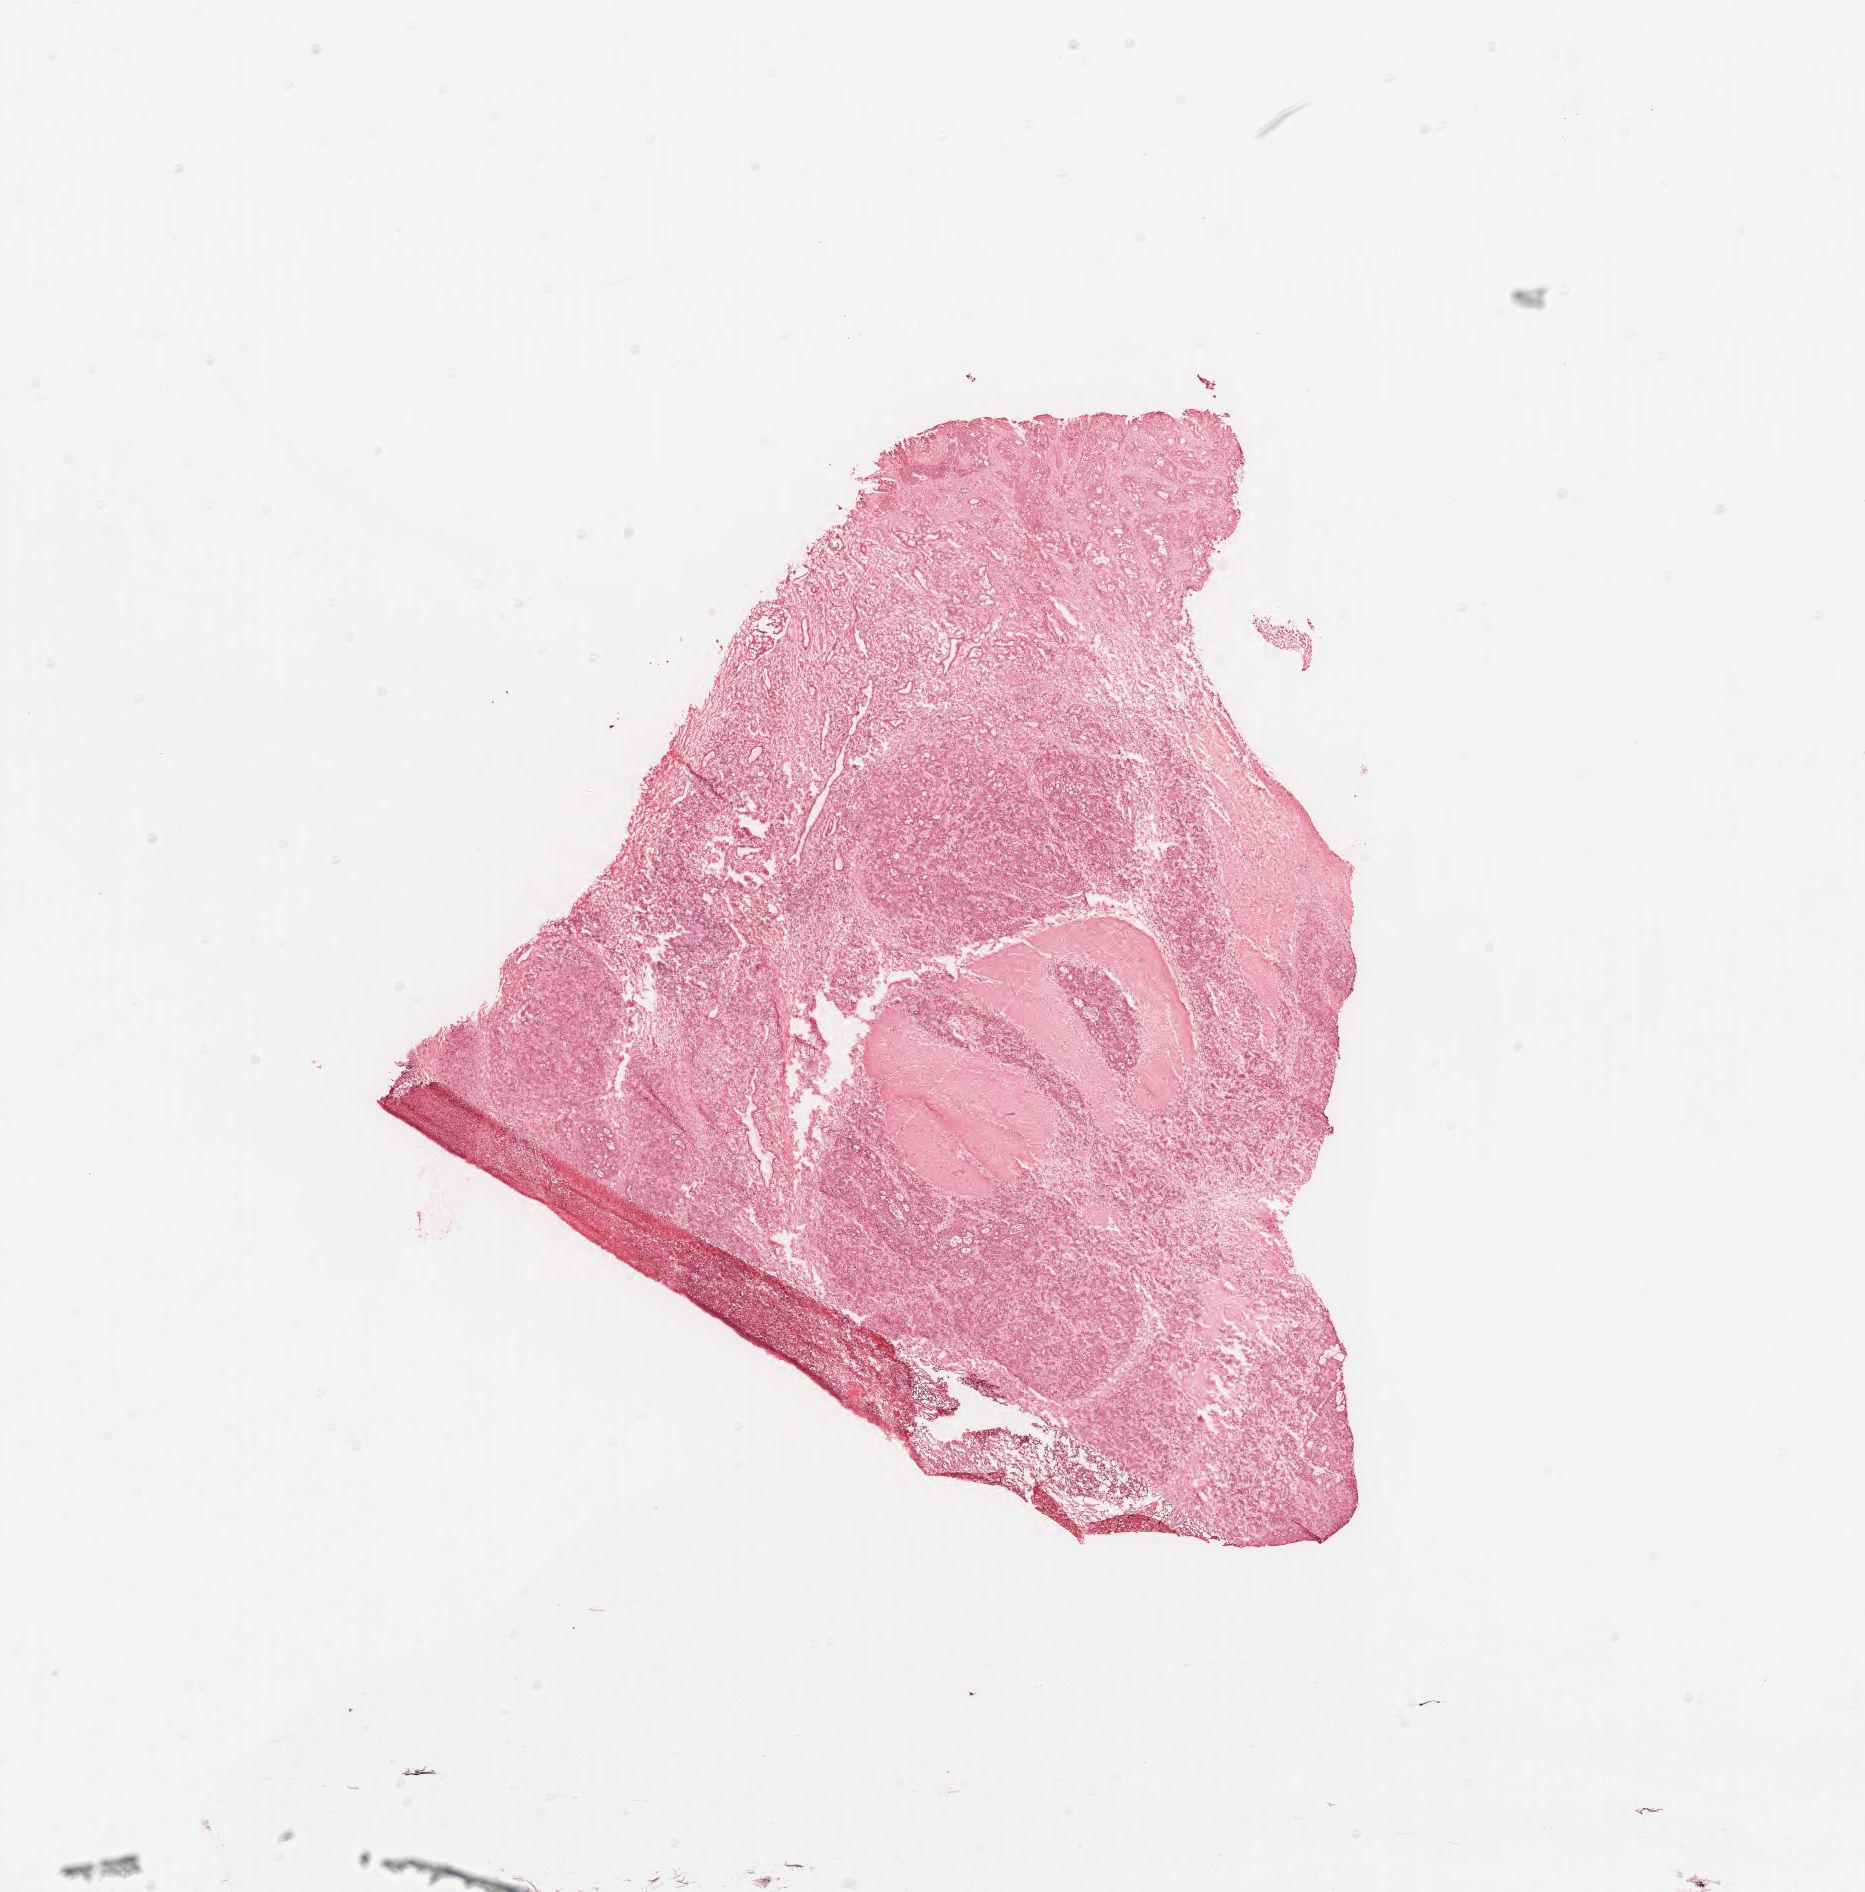
Digitized haematoxylin and eosin-stained section — a low-resolution overview of the entire scanned area, about 14.7 x 14.9 mm. Frozen section. Specimen: primary tumor. Patient: male, age at initial diagnosis 56 years. Tumor grade: G3 (poorly differentiated). Pathologist review of this section (percent, as recorded): tumor cells 58%, tumor nuclei 90%, stromal cells 20%, necrosis 20%, normal cells 2%. Infiltration values recorded for this section: lymphocyte infiltration 0%, monocyte infiltration 0%, neutrophil infiltration 0%.
AJCC pathologic stage: Stage IIIB. Histologic diagnosis: Adenocarcinoma, metastatic, NOS.